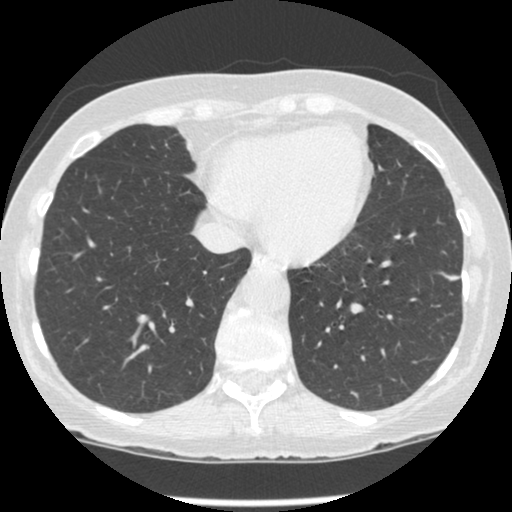
Low-dose screening chest CT, one axial slice; slice 73 of 247 in the series (ordered by position); reconstruction kernel STANDARD; lung window (W 1500 / L -600 HU); 1.25 mm slice thickness; 512 × 512 image matrix, field of view 303 × 303 mm.
Structures marked on this image (expert manual segmentation):
- lesion 1 (tumor, lower lobe of left lung): bounding box <444,274,459,281> (left, top, right, bottom; pixels)